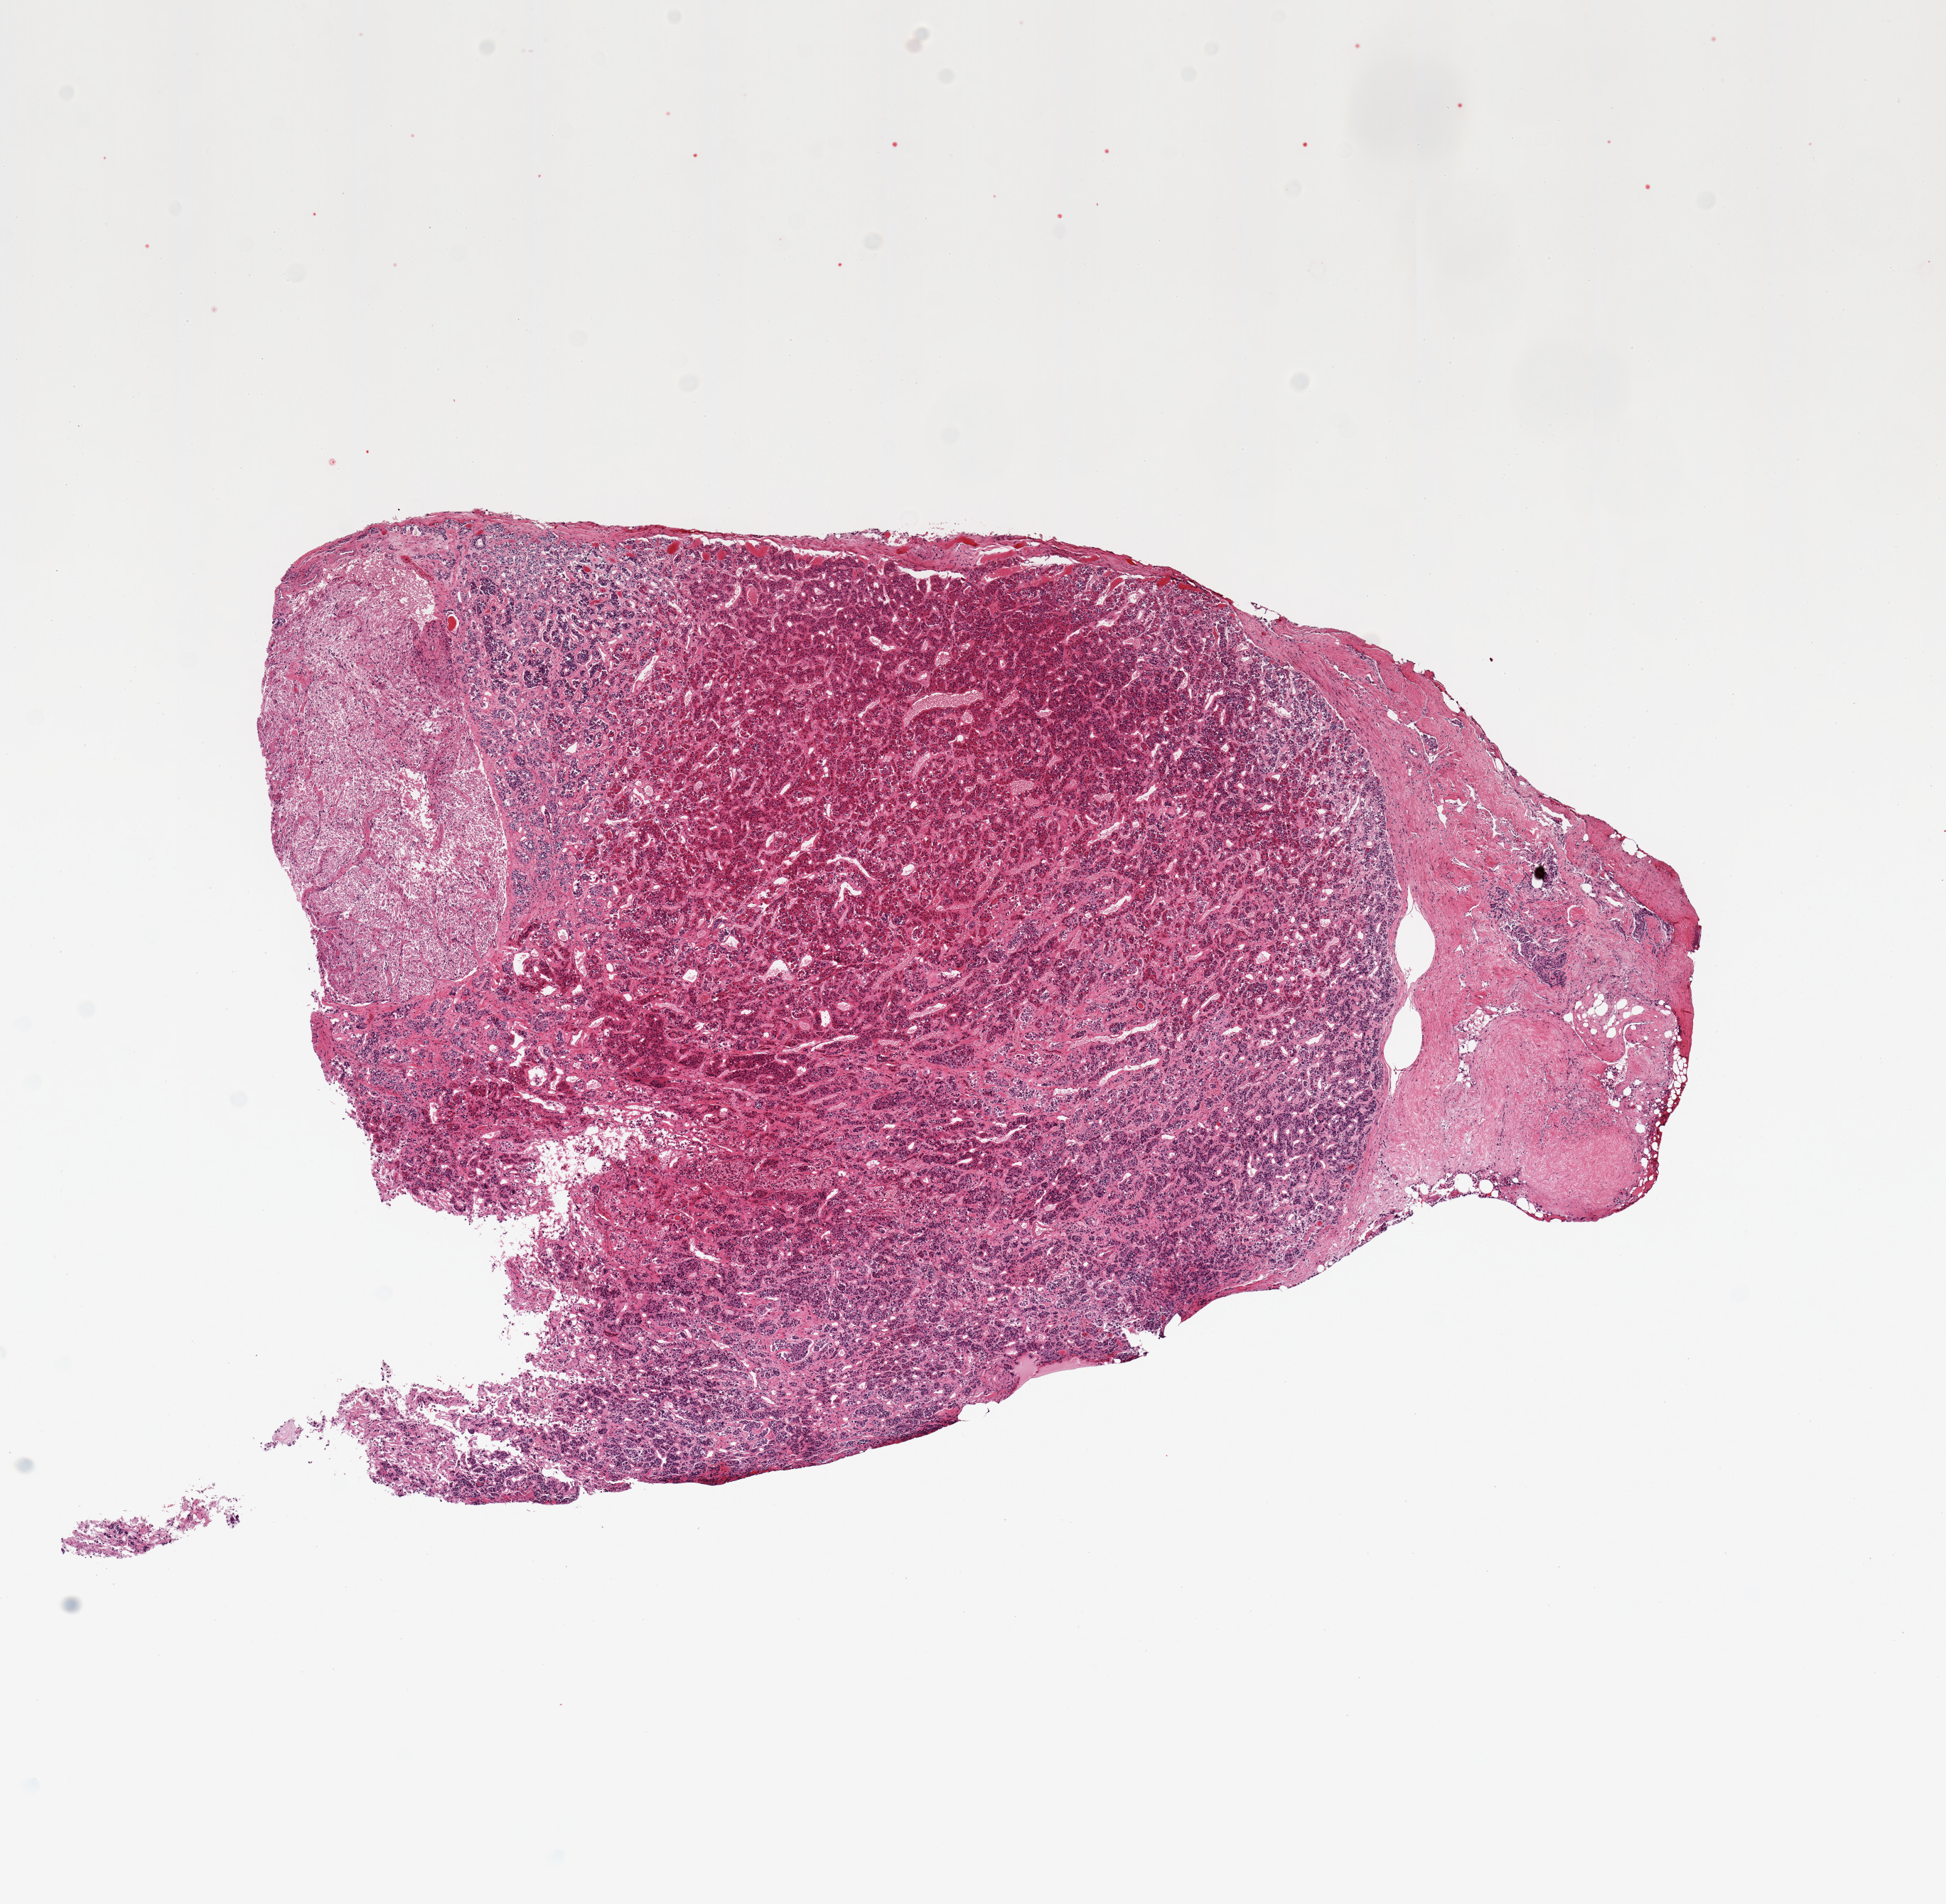
Whole-slide image, hematoxylin and eosin (H&E) stain, low-resolution overview of the scanned area, about 10.8 x 10.6 mm (acquisition: 20x scan); PAXgene-fixed, paraffin-embedded tissue; section of pituitary (target tissue); tissue donor sample. Donor sex: male.
Review note (as recorded): 1 piece; adenohypophysis and neurohypophysis; dura with meningeal rest and psammoma bodies.